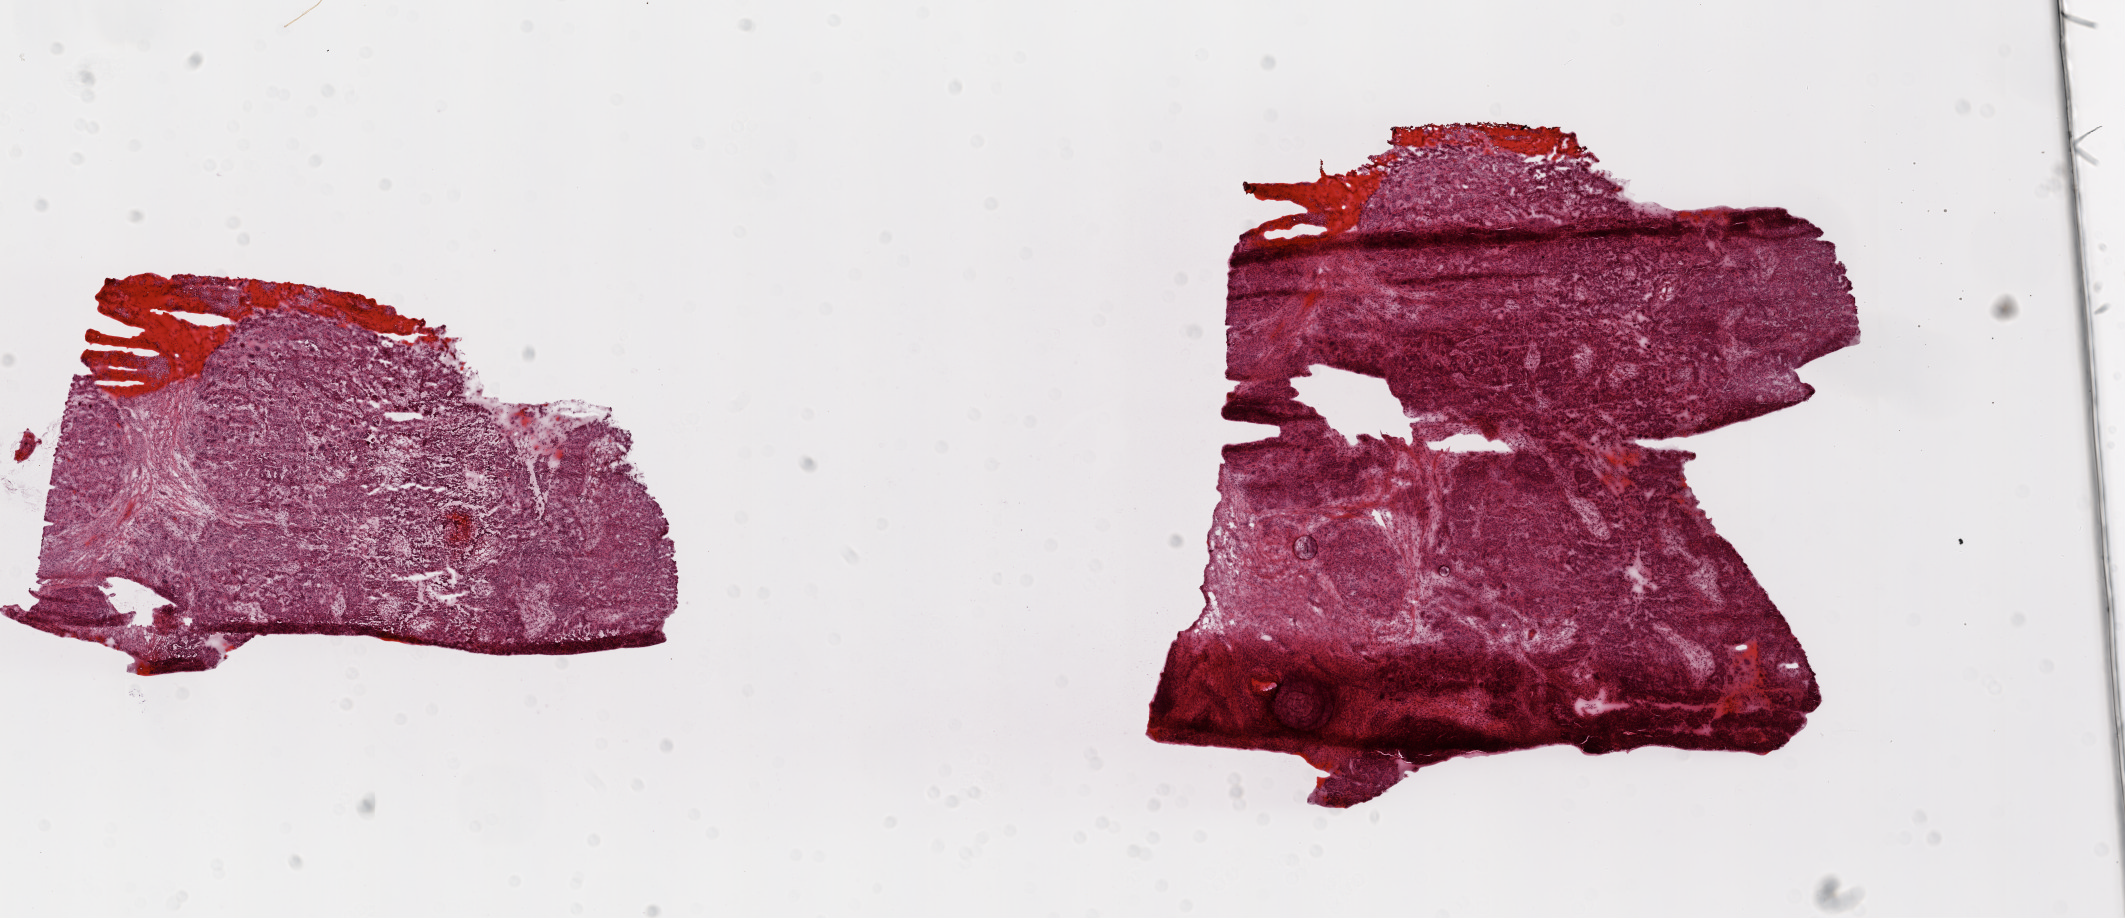
H&E-stained whole-slide image — whole scanned area (about 17.1 x 7.4 mm, slide scanned at 20x) shown as a low-resolution overview. Frozen section from the top of the tissue portion. Ovary, primary tumour sample. Female patient; age at initial diagnosis 45 years. Histologic grade: G3 (poorly differentiated). Slide review estimates, as recorded: tumour cells 90%, tumour nuclei 90%, normal cells 0%, stromal cells 10%, necrosis 0%. Inflammatory infiltration, as recorded: lymphocyte infiltration 0%, monocyte infiltration 0%, neutrophil infiltration 0%.
Diagnosis: Serous cystadenocarcinoma, NOS. Laterality: bilateral. FIGO stage: IV.